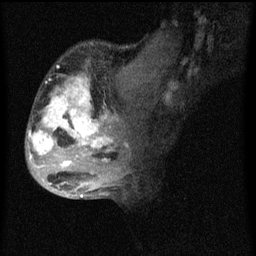
Breast MRI (dynamic contrast-enhanced), one sagittal slice. Position 27 of 60 along the scan axis. Dynamic contrast-enhanced series, image 2 of 4 at this slice position (ordered by acquisition). 1.5 T. TE 4.2 ms, TR 8 ms. 2 mm slice thickness. 256 × 256 image matrix. Female patient, age 50 years.
Outlined on this slice (semi-automatic segmentation, software-assisted and operator-edited):
- analysis volume of interest (the breast-tissue region the enhancement analysis was run in; not a lesion): box from (x=26, y=46) to (x=124, y=177) px
- tumour enhancement mask (voxels above the 70 % enhancement threshold inside the analysis volume of interest): (x=29, y=78)–(x=114, y=169)